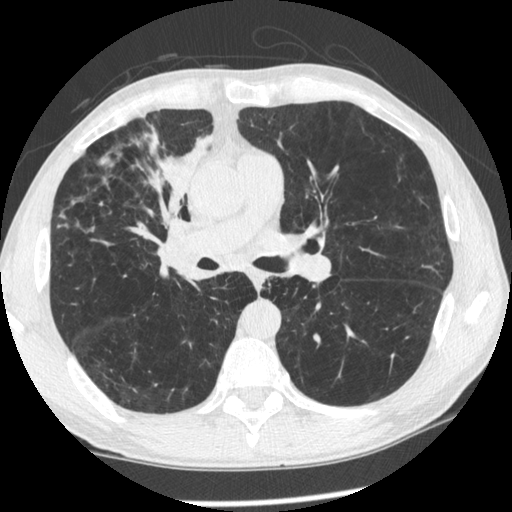
Low-dose screening chest CT, one axial slice; position 134 of 261 along the scan axis; 120 kVp; lung window (W 1500 / L -600 HU); 1.25 mm slice thickness; 512 × 512 image matrix, field of view 340 × 340 mm.
Structures marked on this image (outlined manually by an expert reader):
- lesion 1 (tumor, upper lobe of right lung): box from (x=144, y=126) to (x=213, y=236) px